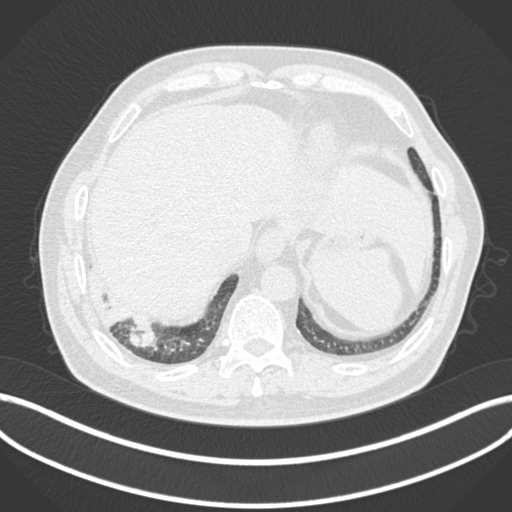
Chest CT, one axial slice. Lung window (W 1500 / L -600 HU). 512 × 512 image matrix, field of view 400 × 400 mm. Patient: male, 59 years.
Structures marked on this image (rectangle marked by the reading radiologist):
- lung tumour (recorded histology: adenocarcinoma): bounding box [x1, y1, x2, y2] px = [128, 319, 160, 351]